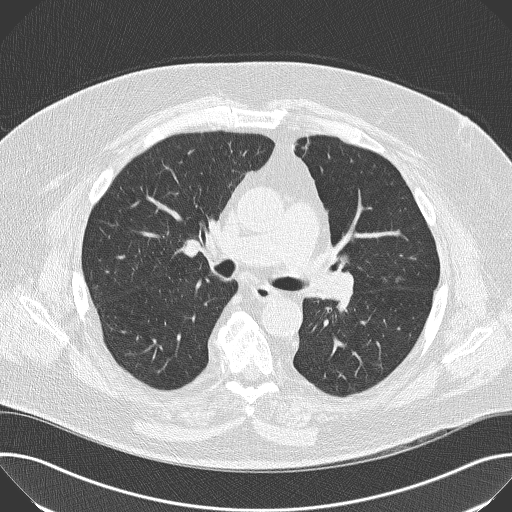
Chest CT (low-dose screening protocol), one axial image; baseline annual screen; lung window (W 1500 / L -600 HU); 2 mm slice thickness; 120 kVp. Male, age 68 years at enrolment. Former smoker at enrolment.
Expert reader's lesion annotation, box from (x=317, y=235) to (x=367, y=283) px. The screening reader recorded 2 non-calcified nodules or masses ≥4 mm on this exam; which of them this box marks is not recorded. Lung cancer was diagnosed 638 days after this screen: squamous cell carcinoma, NOS, left upper lobe, poorly differentiated (G3), stage IIB (AJCC 6th edition), 35 mm at pathology.